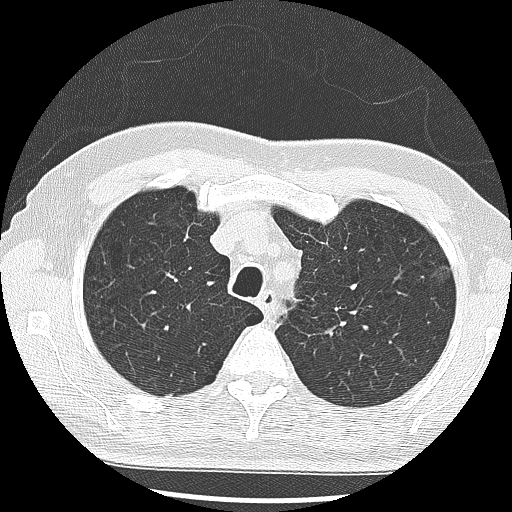
Low-dose screening chest CT, one axial slice. Slice 224 of 285 in the series (ordered by position). Reconstruction kernel LUNG. 120 kVp. Lung window (W 1500 / L -600 HU). 2.5 mm slice thickness. 512 × 512 image matrix, field of view 340 × 340 mm.
Annotated regions visible in this slice (outlined manually by an expert reader):
- lesion 1 (tumor, upper lobe of left lung): bounding box (x1, y1, x2, y2) in pixels: (431, 266, 449, 278)